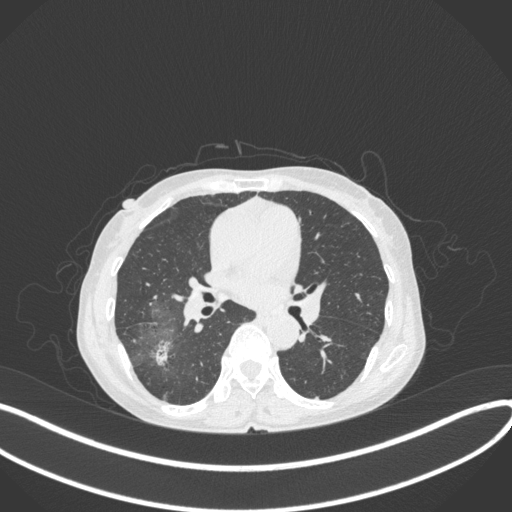
Chest CT, one axial slice; slice 208 of 379 in the series (ordered by position); lung window (W 1500 / L -600 HU); 1 mm slice thickness; 512 × 512 image matrix, field of view 400 × 400 mm. Patient: female, 69 years. From the clinical record (not read from this slice): clinical TNM (as recorded): T1b N0 M0; histopathological grade: G2-3.
Outlined on this slice (rectangle marked by the reading radiologist):
- lung tumour (recorded histology: adenocarcinoma): bounding box <147,332,175,369> (left, top, right, bottom; pixels)